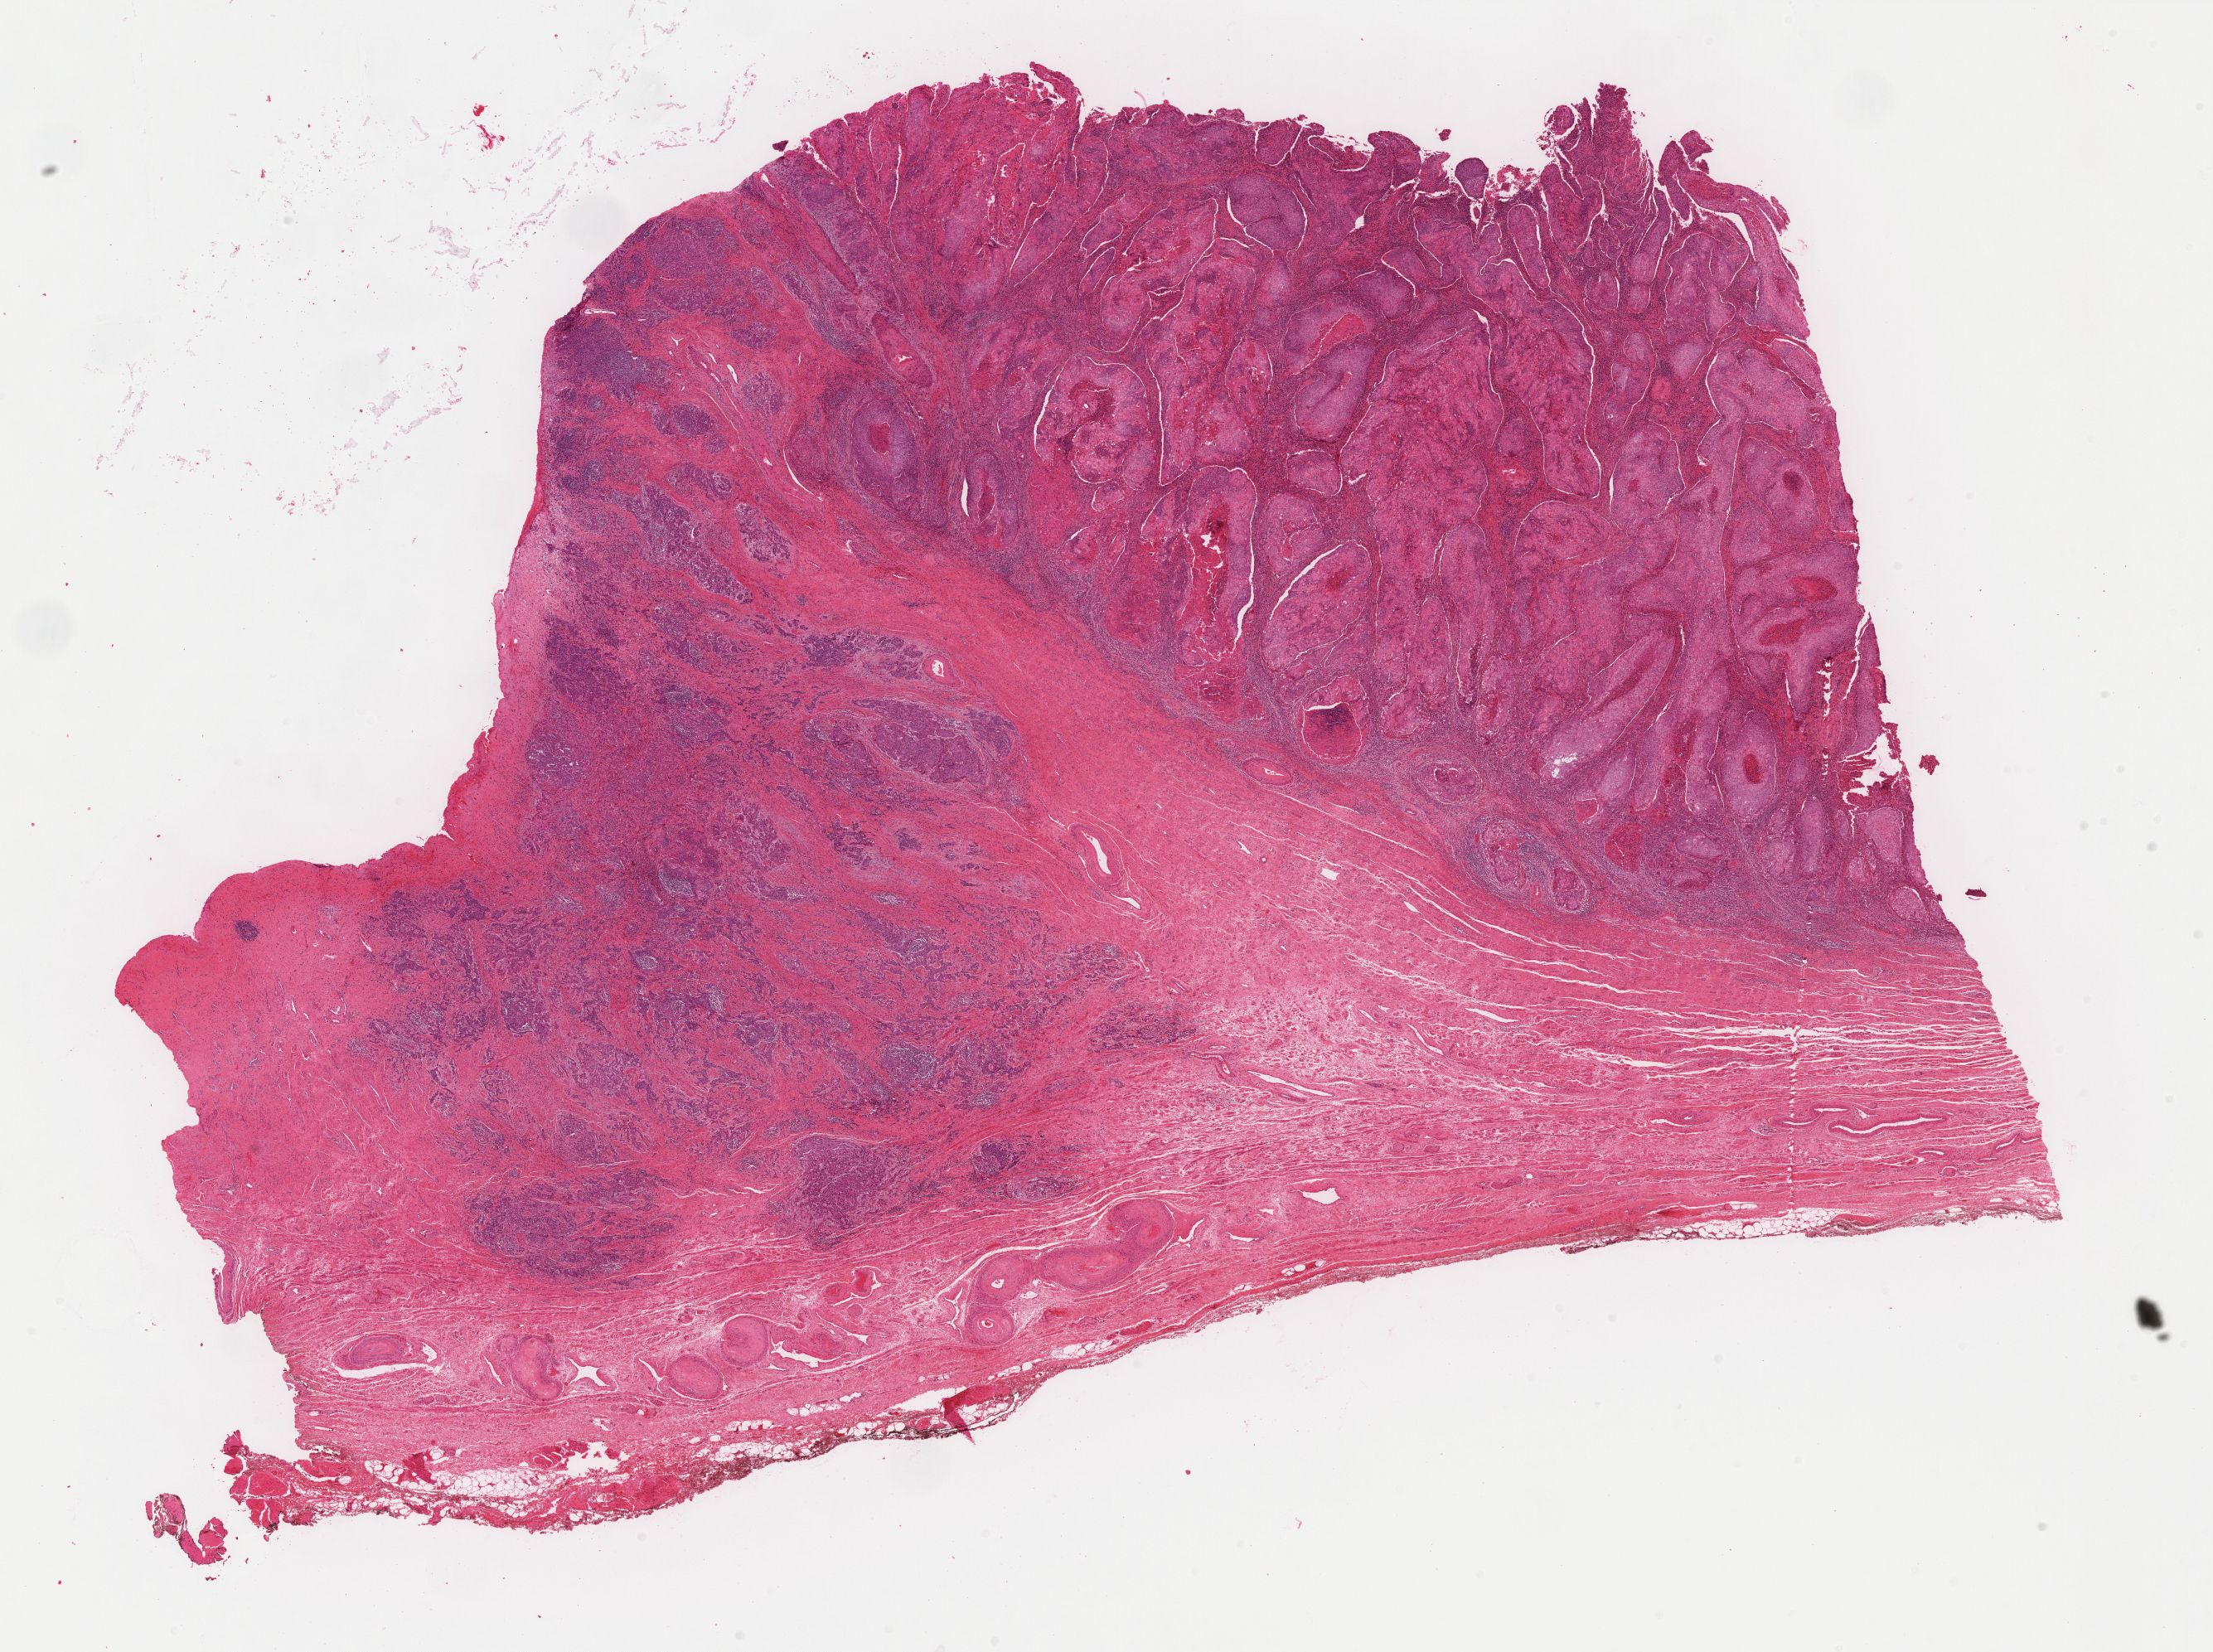
Digitized H&E tissue section (whole slide), shown as a low-resolution overview of the whole scanned area (about 21.4 x 16.0 mm); formalin-fixed paraffin-embedded (FFPE) diagnostic section; cervix, primary tumour sample. Patient: female, age at initial diagnosis 78 years.
Pathologic diagnosis: Squamous cell carcinoma, NOS (cervix uteri).